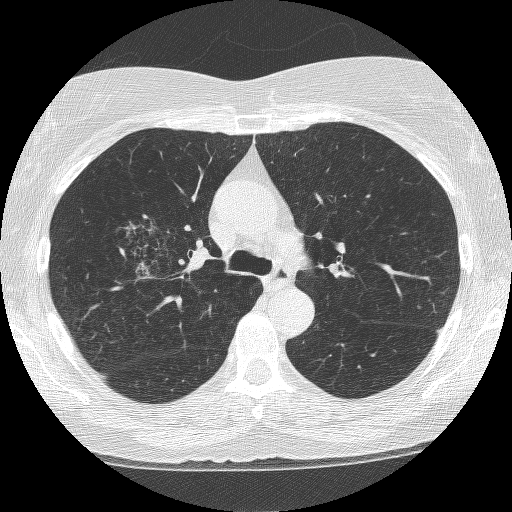
Chest CT (low-dose screening protocol), one axial image; second annual screen; lung window (W 1500 / L -600 HU); 1.25 mm slice thickness; lung (sharp) reconstruction kernel (BONE); 512 × 512 image matrix. Female, age 64 years at enrolment. Former smoker at enrolment.
• Expert-annotated lung lesion, bounding box [x1, y1, x2, y2] px = [114, 204, 210, 293].
• The screening reader recorded 4 non-calcified nodules or masses ≥4 mm on this exam (right upper lobe, right upper lobe, right upper lobe, left upper lobe); which of them this box marks is not recorded.
• Official screen result: positive, other.
• Participant outcome: lung cancer diagnosed 381 days after this screen — adenocarcinoma, NOS, right upper lobe, right middle lobe, right hilum, stage IV (AJCC 6th edition), 85 mm at pathology.